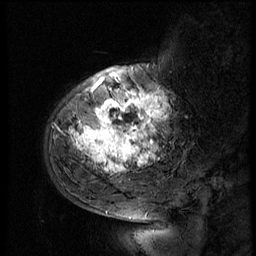
Breast MRI (dynamic contrast-enhanced), one sagittal slice. Slice 15 of 56 in the series (ordered by position). 3 images stored at this slice position (order not interpretable as contrast timing). 1.5 T. TE 4.2 ms, TR 9 ms. 2.5 mm slice thickness. 256 × 256 image matrix, field of view 180 × 180 mm. Female patient, age 51 years. From the clinical record (not read from this slice): setting: breast cancer imaged before/during neoadjuvant chemotherapy; receptor status: triple-negative.
Structures marked on this image (semi-automatically segmented with operator editing):
- analysis volume of interest (the breast-tissue region the enhancement analysis was run in; not a lesion): bounding box <52,66,183,179> (left, top, right, bottom; pixels)
- tumour enhancement mask (voxels above the 140 % enhancement threshold inside the analysis volume of interest): <72,78,169,175>